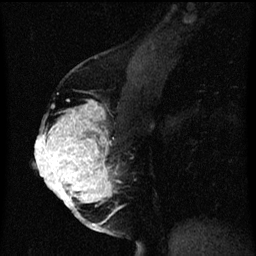
Breast MRI (dynamic contrast-enhanced), one sagittal slice; position 32 of 60 along the scan axis; dynamic contrast-enhanced series, image 2 of 3 at this slice position (ordered by acquisition); 1.5 T; TE 4.2 ms, TR 8 ms; 256 × 256 image matrix, field of view 180 × 180 mm. Patient: female, 56 years.
Outlined on this slice (semi-automatically segmented with operator editing):
- analysis volume of interest (the breast-tissue region the enhancement analysis was run in; not a lesion): box from (x=40, y=100) to (x=123, y=209) px
- tumour enhancement mask (voxels above the 70 % enhancement threshold inside the analysis volume of interest): (x=40, y=100)–(x=117, y=209)